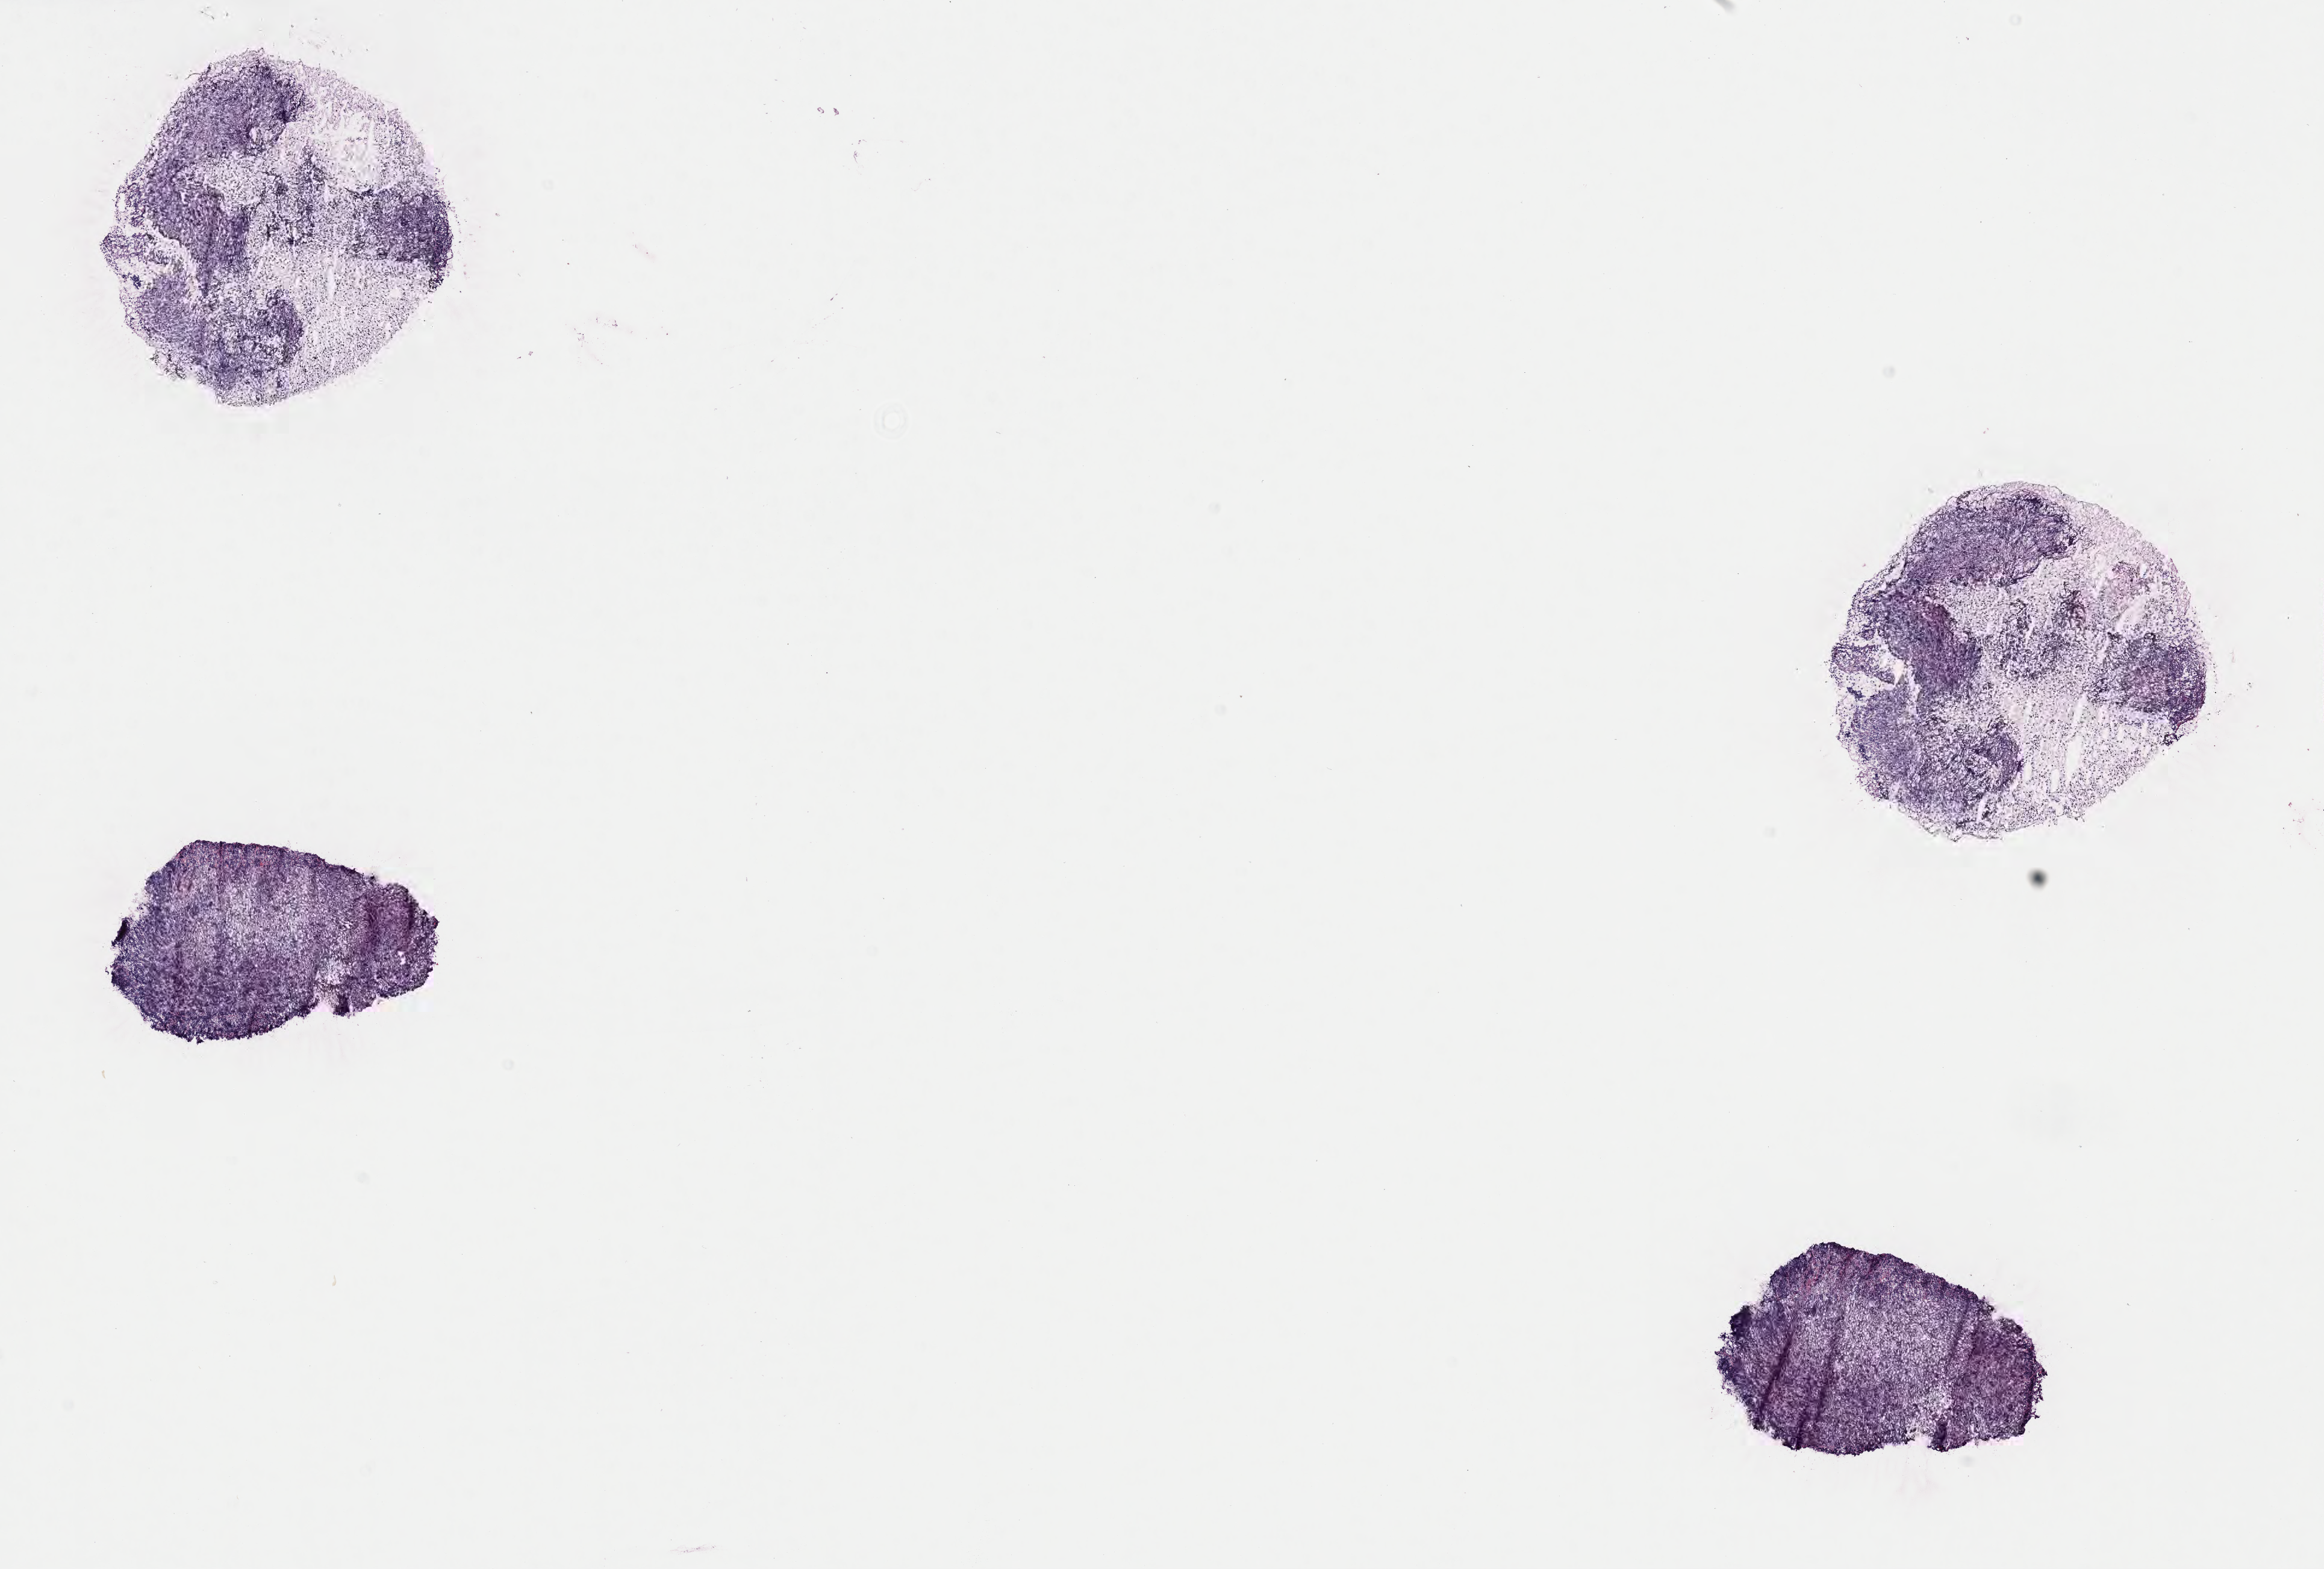
Whole-slide image, haematoxylin and eosin stain, low-resolution overview of the scanned area, about 15.6 x 10.5 mm, frozen section (tissue freezing medium), specimen: primary tumor, site: mandible. Female, age 8 years at initial diagnosis. Composition of this section per pathologist review: tumor cells 60%, tumor nuclei 80%, stromal cells 5%, necrosis 35%, normal cells 0%. Infiltration values recorded for this section: lymphocyte infiltration 30%, monocyte infiltration 40%, neutrophil infiltration 10%.
Ann Arbor stage (patient): Stage II. Diagnosis: Burkitt lymphoma, NOS.